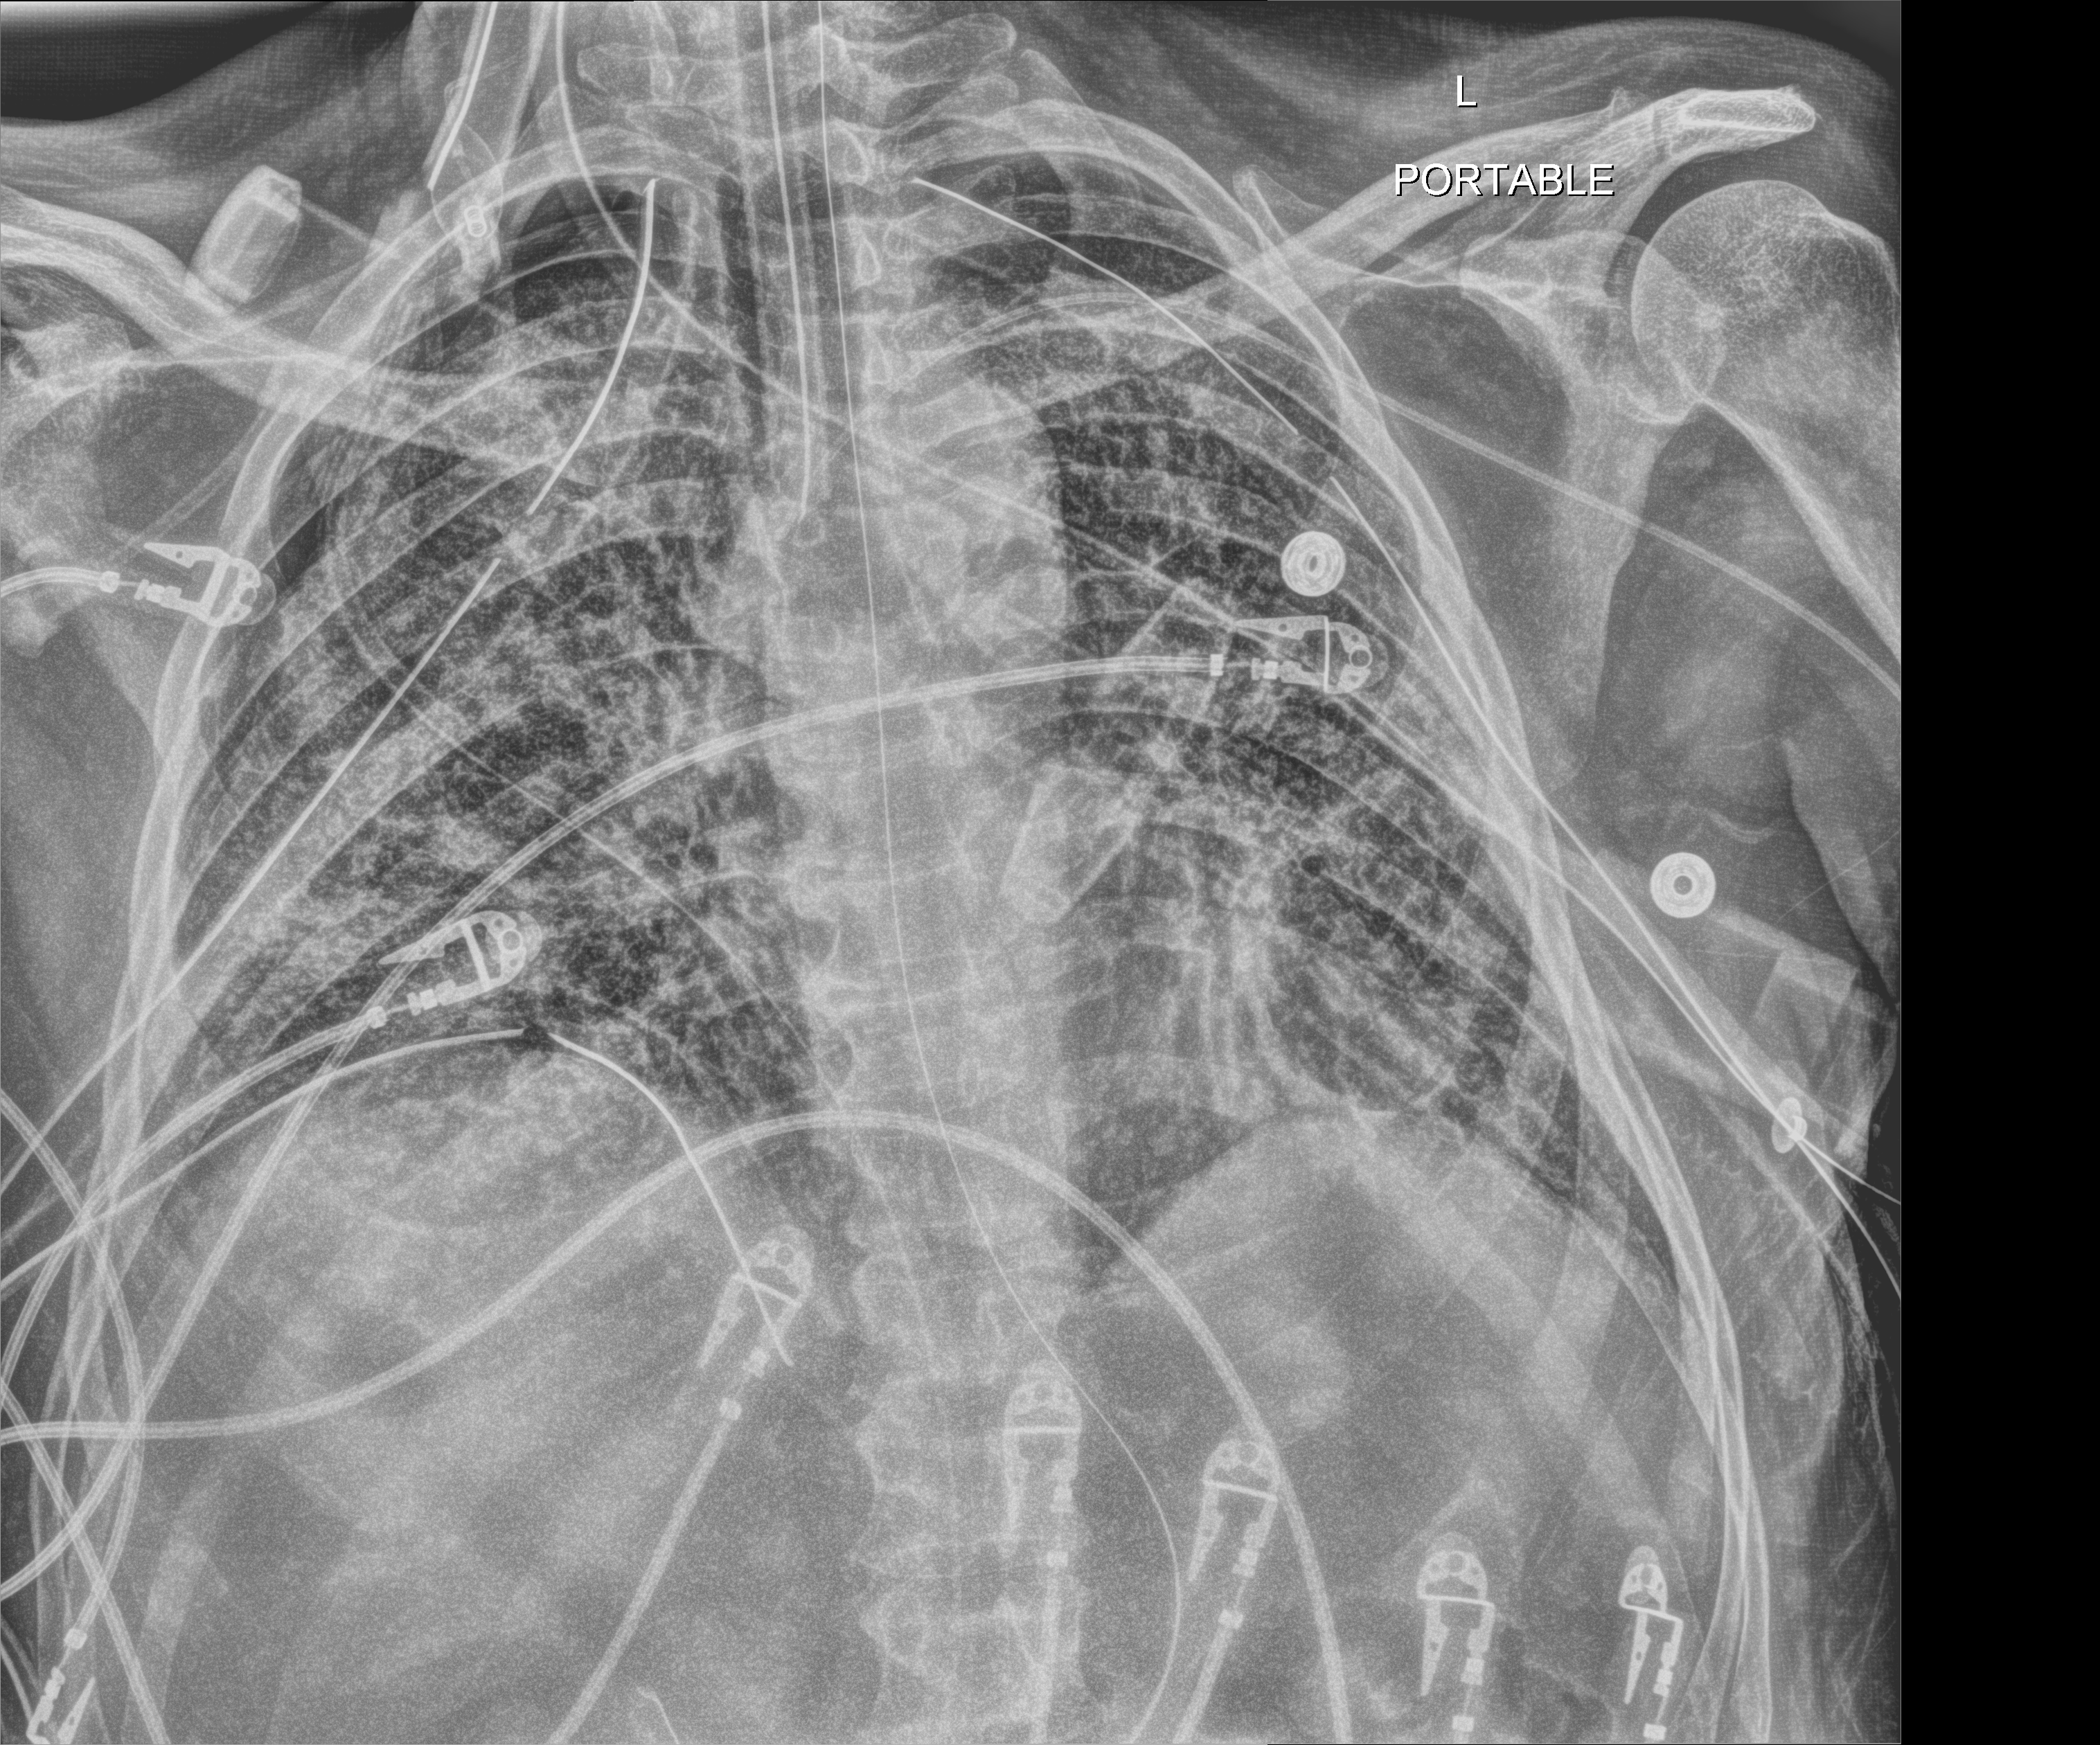
Portable chest radiograph; anteroposterior (AP) projection. Male patient hospitalised with COVID-19, age 18–59 years.
From the hospital-stay record, not from the radiograph (when in the stay this image was taken is not recorded):
- admitted to intensive care during this hospital stay: yes